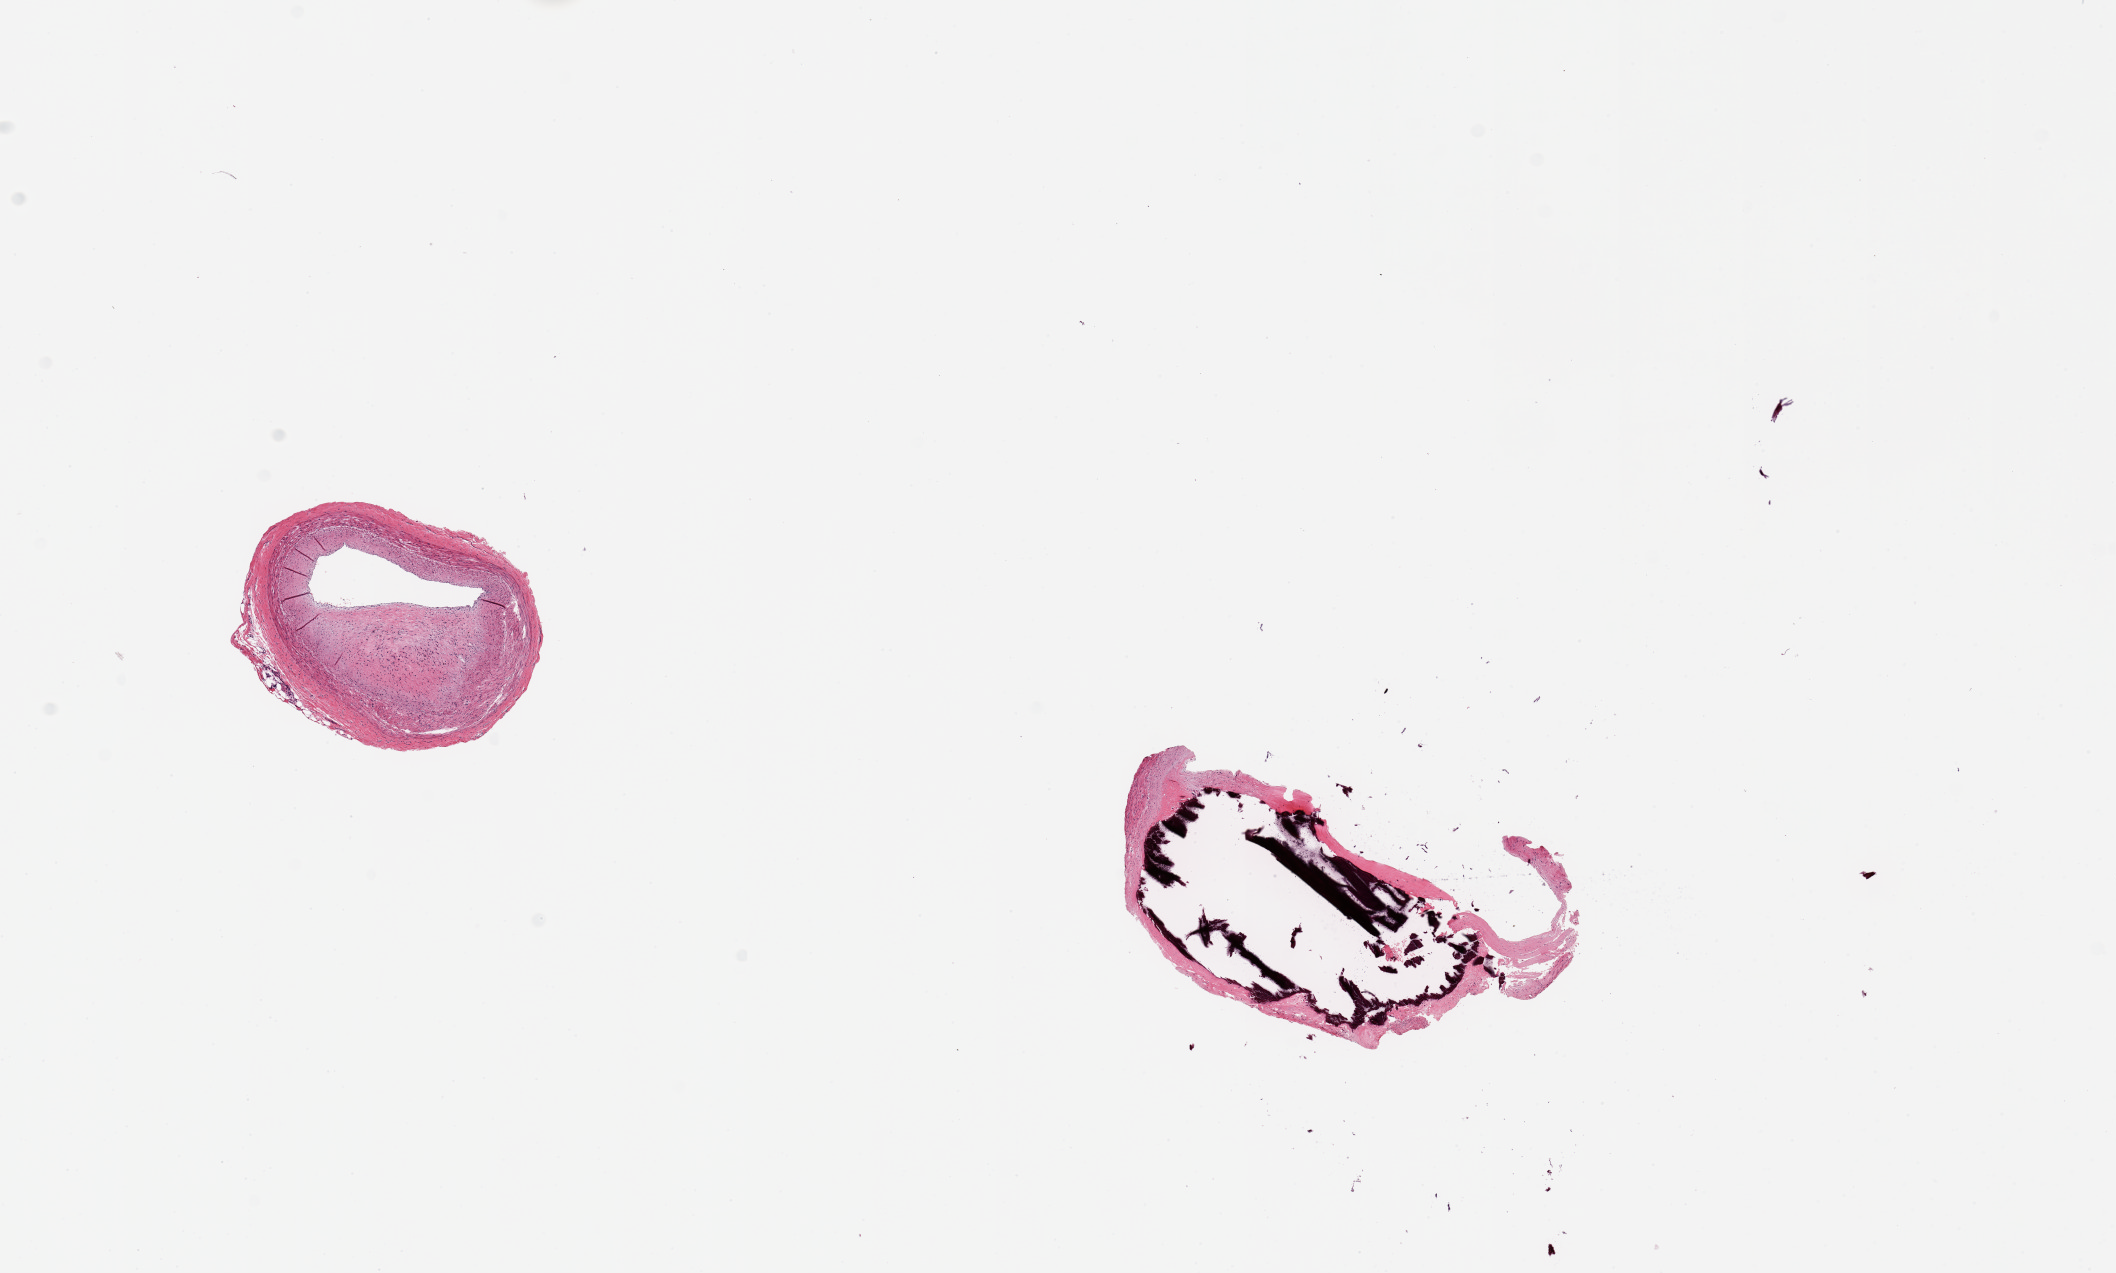
Digitized haematoxylin and eosin-stained section, brightfield — shown as a low-resolution overview of the whole scanned area (about 16.7 x 10.1 mm), PAXgene-fixed paraffin-embedded (PFPE) section, sampled site (target tissue): coronary artery, tissue donor sample. Donor: female.
Reviewer comment on this tissue sample: 2 pieces; calcific atherosclerosis, one piece is fragmented due to calcification, second has 50-75% narrowing of lumen.